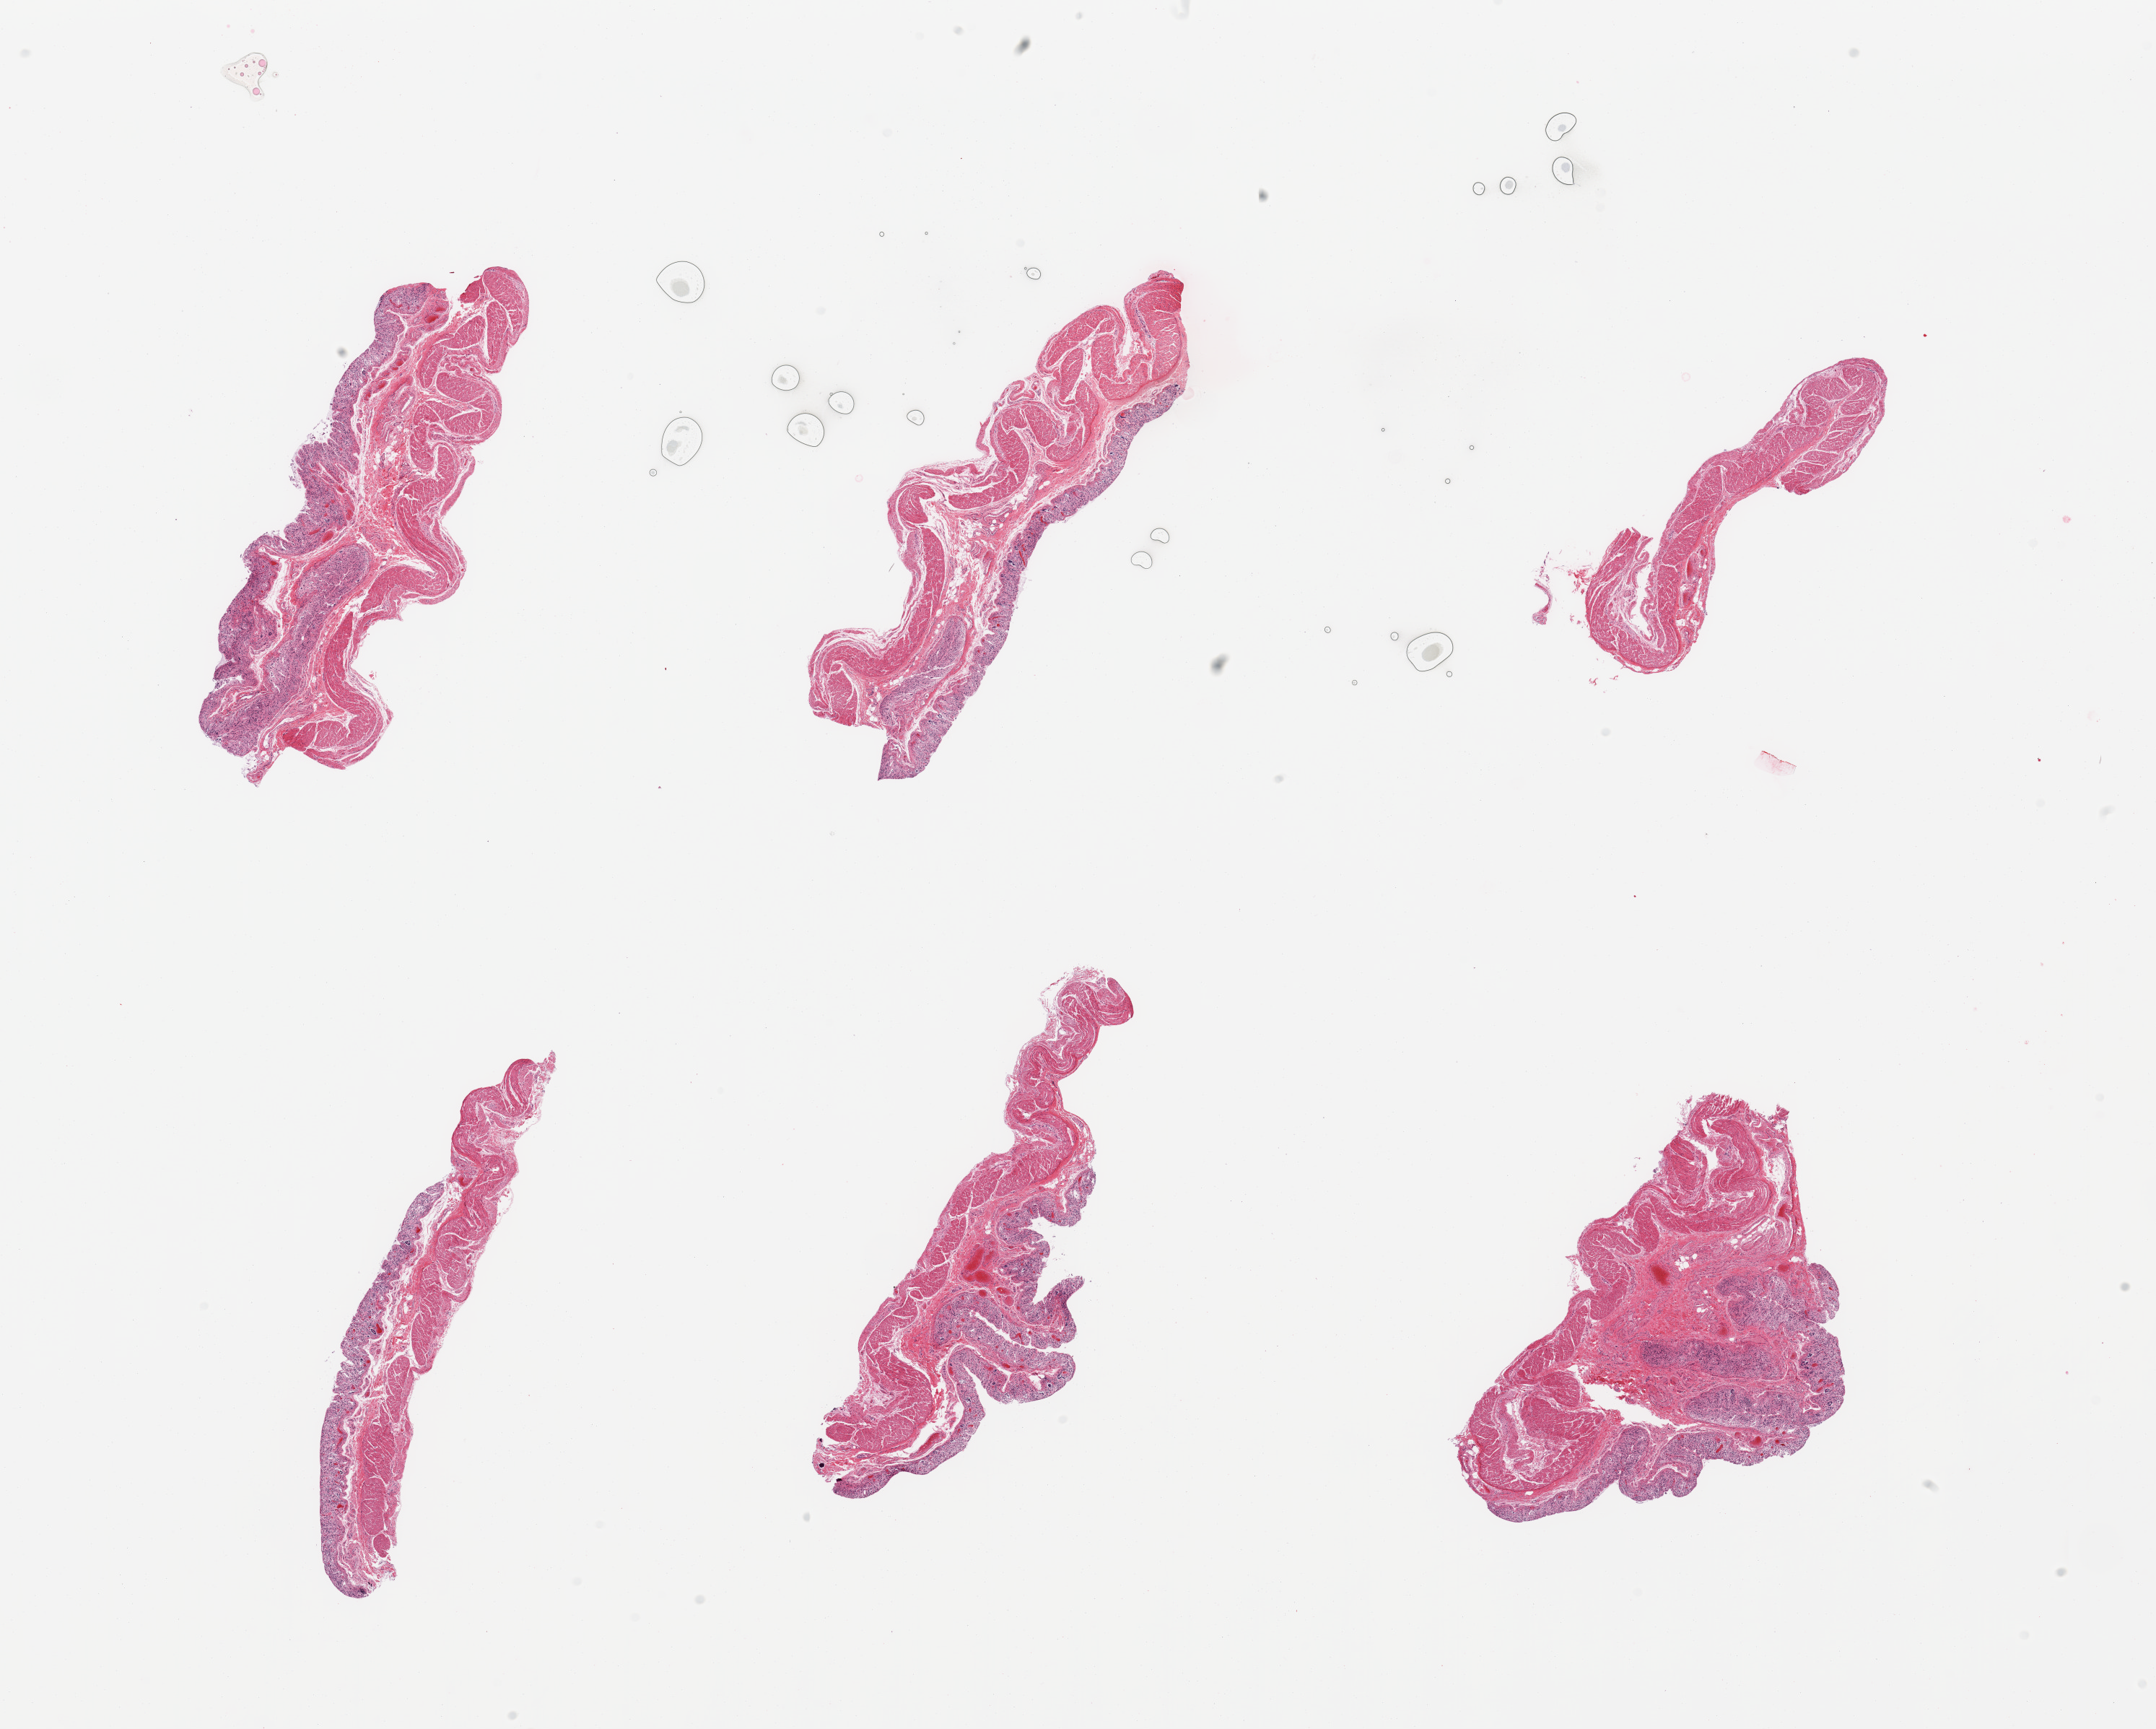
Whole-slide image, hematoxylin and eosin (H&E) stain — shown as a low-resolution overview of the whole scanned area (about 23.6 x 18.9 mm, acquisition: 20x scan).
Specimen: PAXgene-fixed, paraffin-embedded tissue; section of transverse colon (target tissue); tissue donor sample.